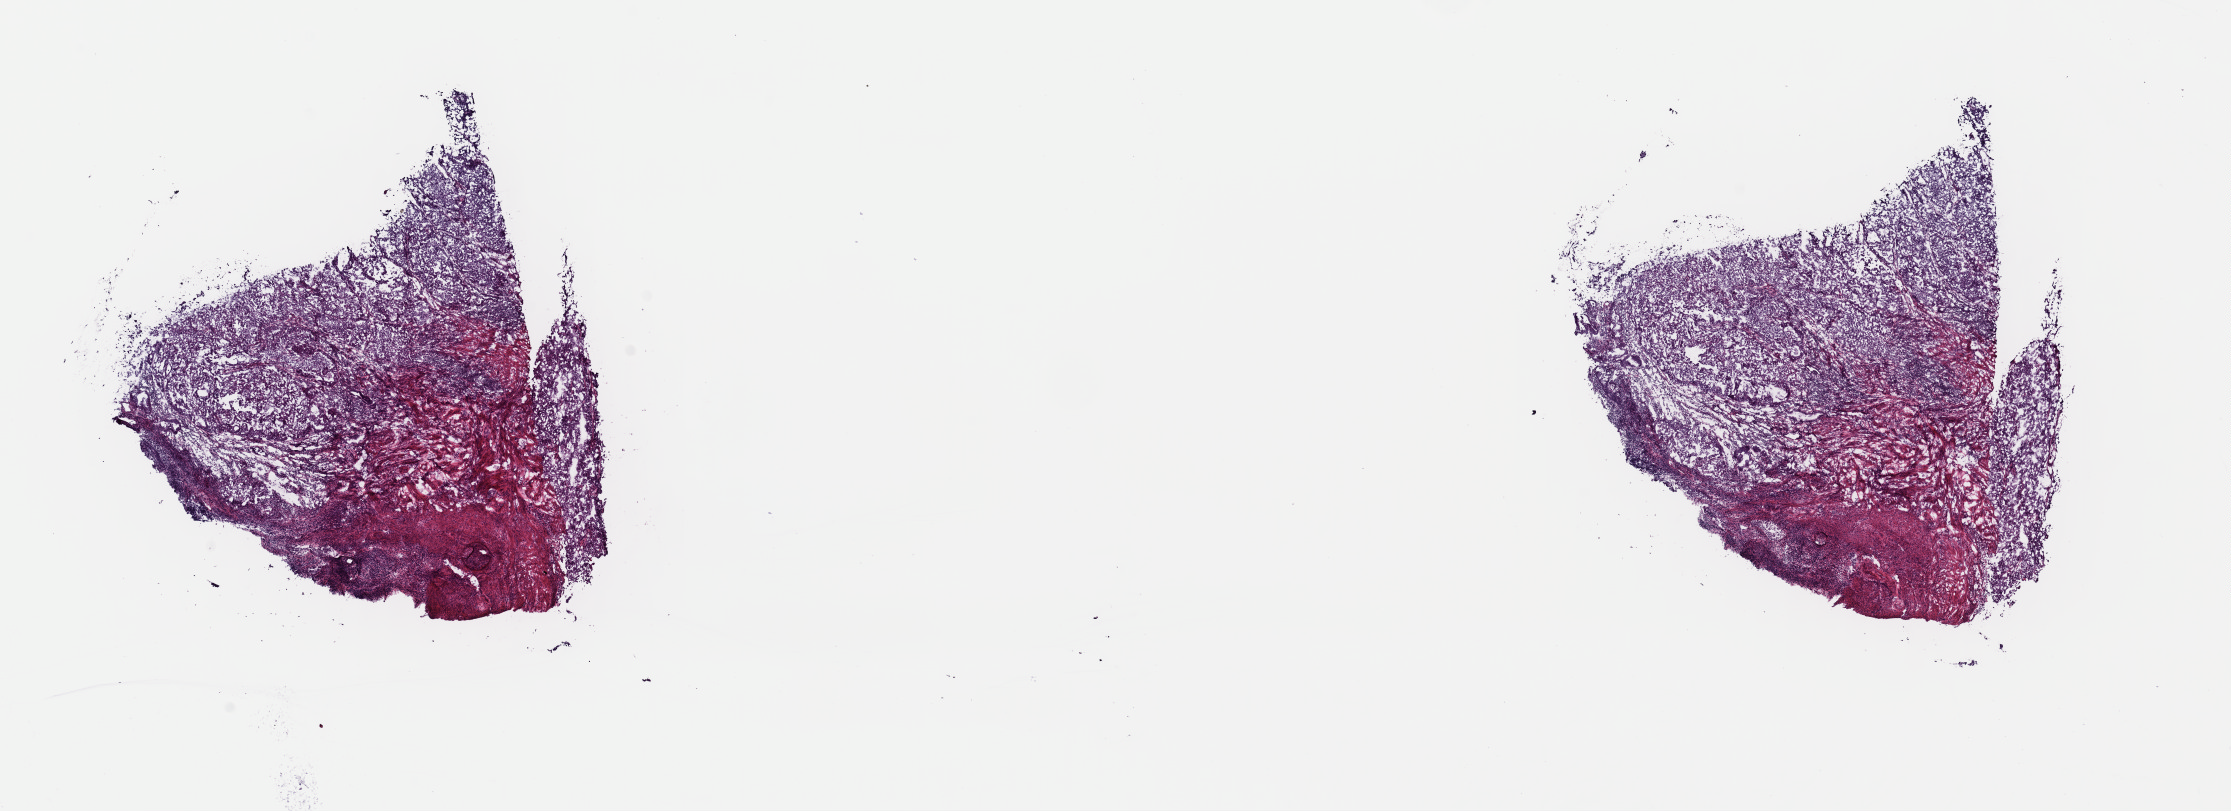
Digitized H&E-stained tissue section (whole slide) — low-resolution overview of the scanned area, about 17.6 x 6.4 mm; frozen section from the top of the tissue portion; sample: primary tumour, uterus. Patient: female, age at initial diagnosis 73 years. Histologic grade: G3 (poorly differentiated). Slide review estimates, as recorded: tumour cells 70%, tumour nuclei 75%, normal cells 30%, stromal cells 0%, necrosis 0%. Inflammatory infiltration, as recorded: lymphocyte infiltration 1%, monocyte infiltration 2%, neutrophil infiltration 0%.
- FIGO stage: IC
- histologic diagnosis: Endometrioid adenocarcinoma, NOS (endometrium)